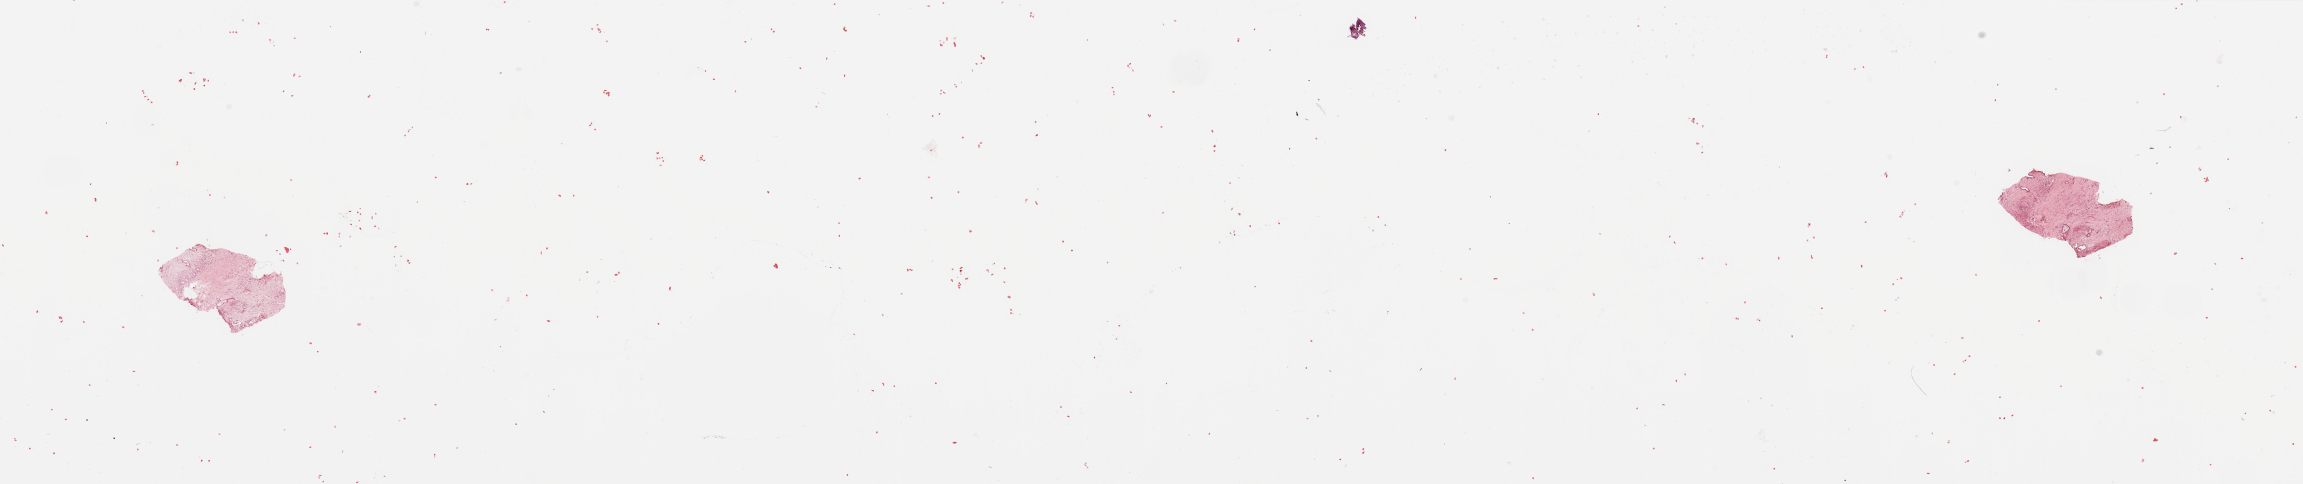
Digitized H&E tissue section (whole slide) — shown as a low-resolution overview of the whole scanned area (about 36.4 x 7.7 mm, slide scanned at 20x); tumour tissue sample, sampled site: pancreas. 63-year-old male patient. Histologic grade: G2 (moderately differentiated). Slide review estimates, as recorded: tumour nuclei 10%, necrosis 2%.
Primary tumour site (as recorded): head. AJCC pathologic stage: IIB. Histologic diagnosis: Infiltrating duct carcinoma, NOS.